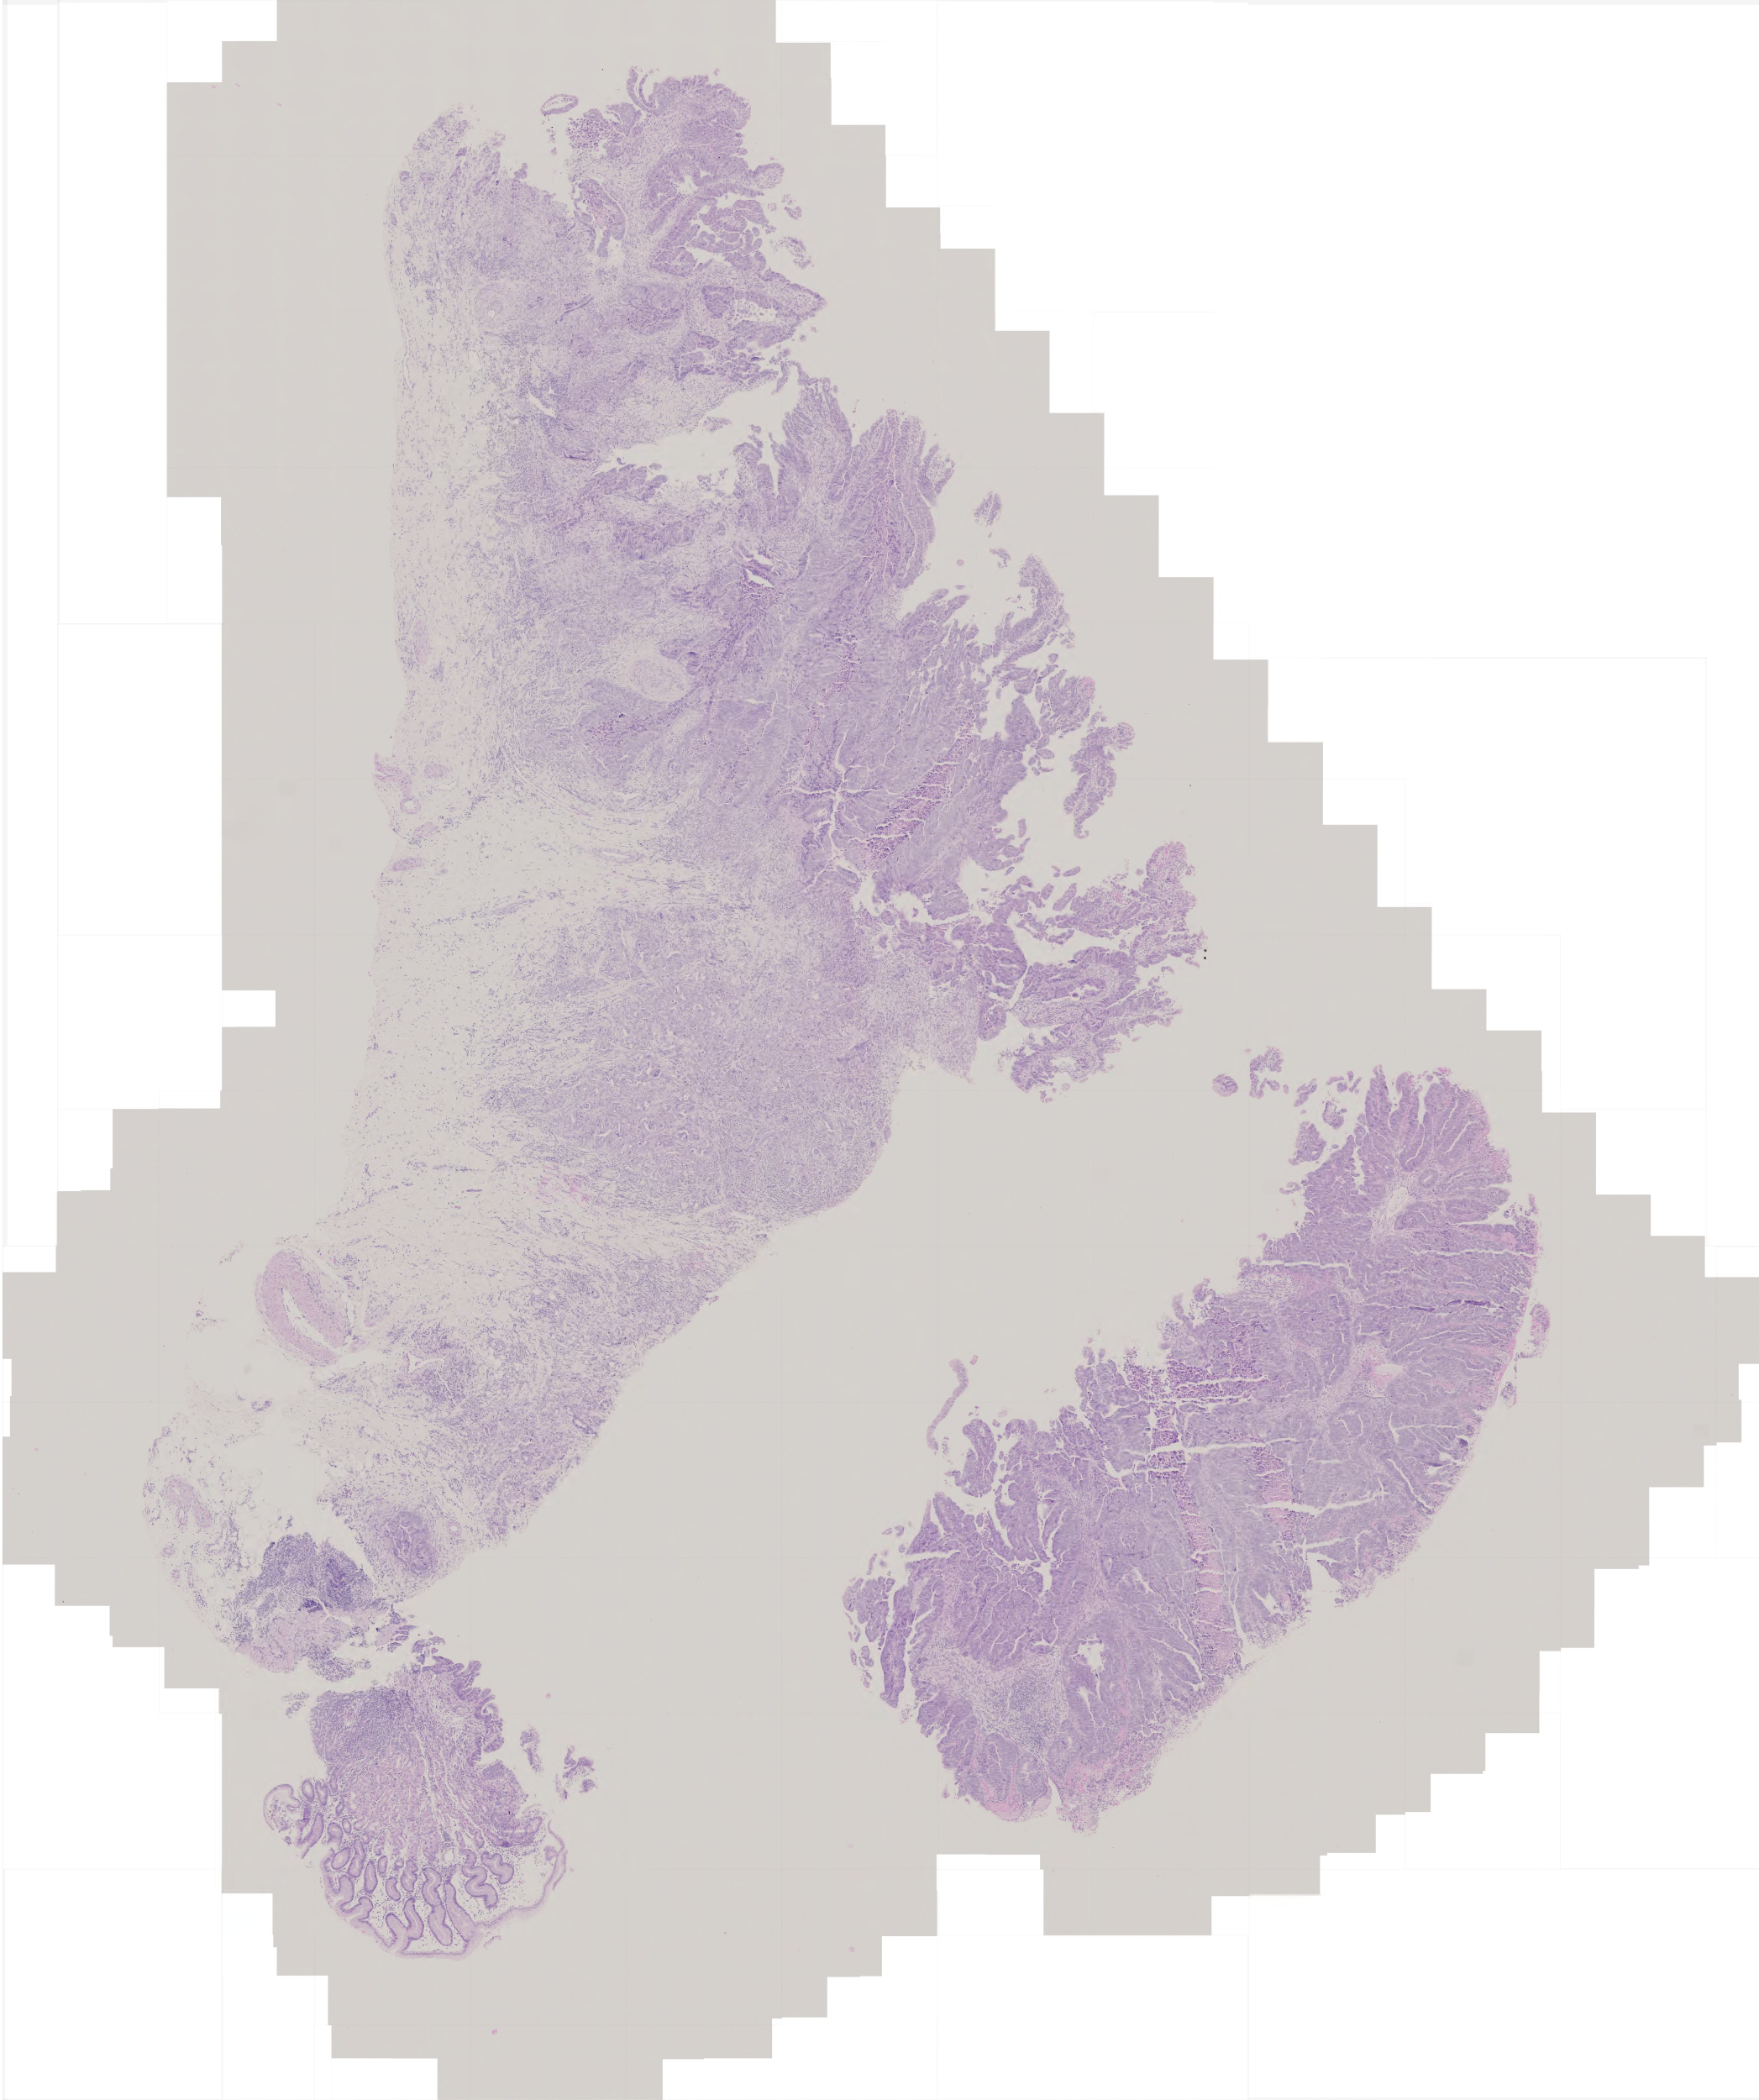
H&E-stained whole-slide image — low-resolution overview of the scanned area, about 4.2 x 5.0 mm; formalin-fixed paraffin-embedded (FFPE) diagnostic section; primary tumour sample from the stomach. Patient: female, age at initial diagnosis 80 years. Histologic grade: G2 (moderately differentiated).
AJCC pathologic stage: IV (5th edition). Pathologic diagnosis: Adenocarcinoma, intestinal type (cardia, NOS).